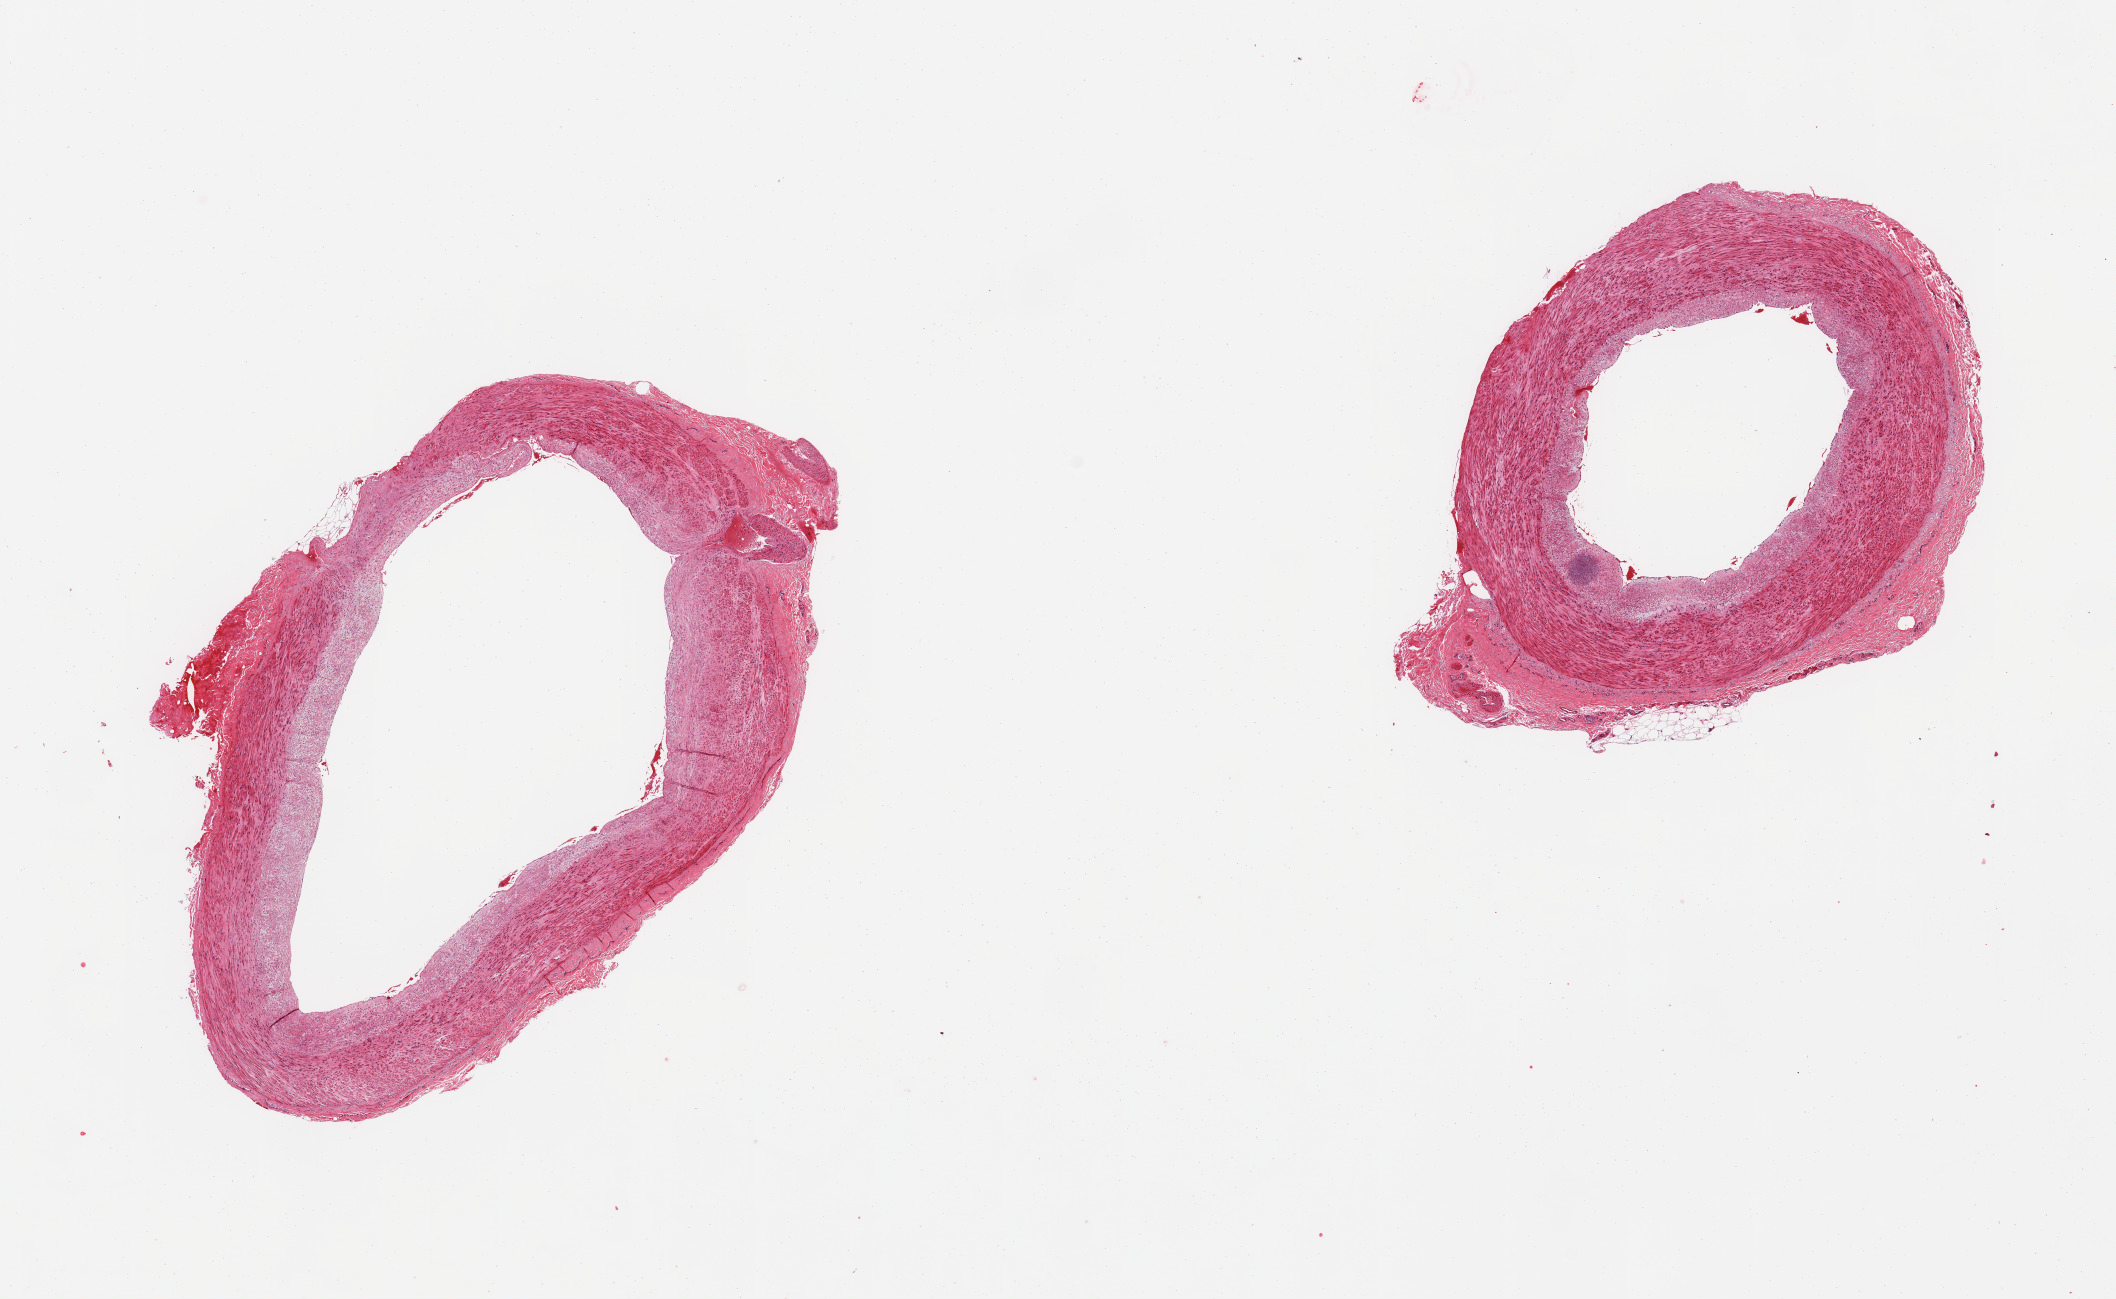
Whole-slide image, haematoxylin and eosin stain, shown as a low-resolution overview of the whole scanned area (about 16.7 x 10.3 mm, from a 20x scan). PAXgene-fixed, paraffin-embedded tissue. Section of tibial artery (target tissue). Donor tissue sample. Male donor.
Pathologist's review note for this sample: 2 pieces; well trimmed, sclerosis.